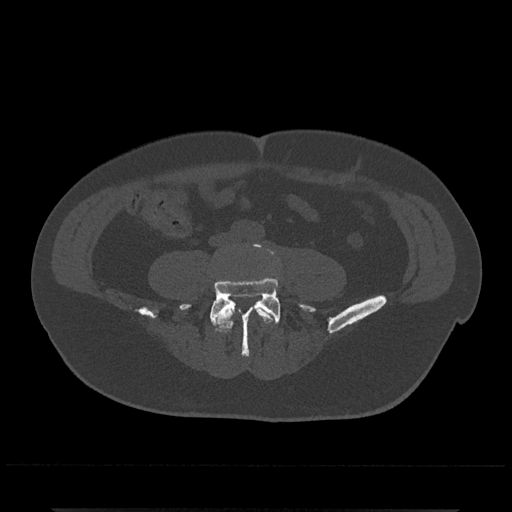
CT including the spine, one axial slice. Position 109 of 797 along the scan axis. Reconstruction kernel Br40s/3. Bone window (W 1800 / L 400 HU). 0.5 mm slice thickness. 512 × 512 image matrix. Male patient, age 67 years. From the clinical record (not read from this slice): primary cancer: prostate.
Outlined on this slice (semi-automatic segmentation, software-assisted and operator-edited):
- L4 vertebra: box from (x=216, y=302) to (x=277, y=332) px
- L5 vertebra: (x=180, y=243)–(x=315, y=356)